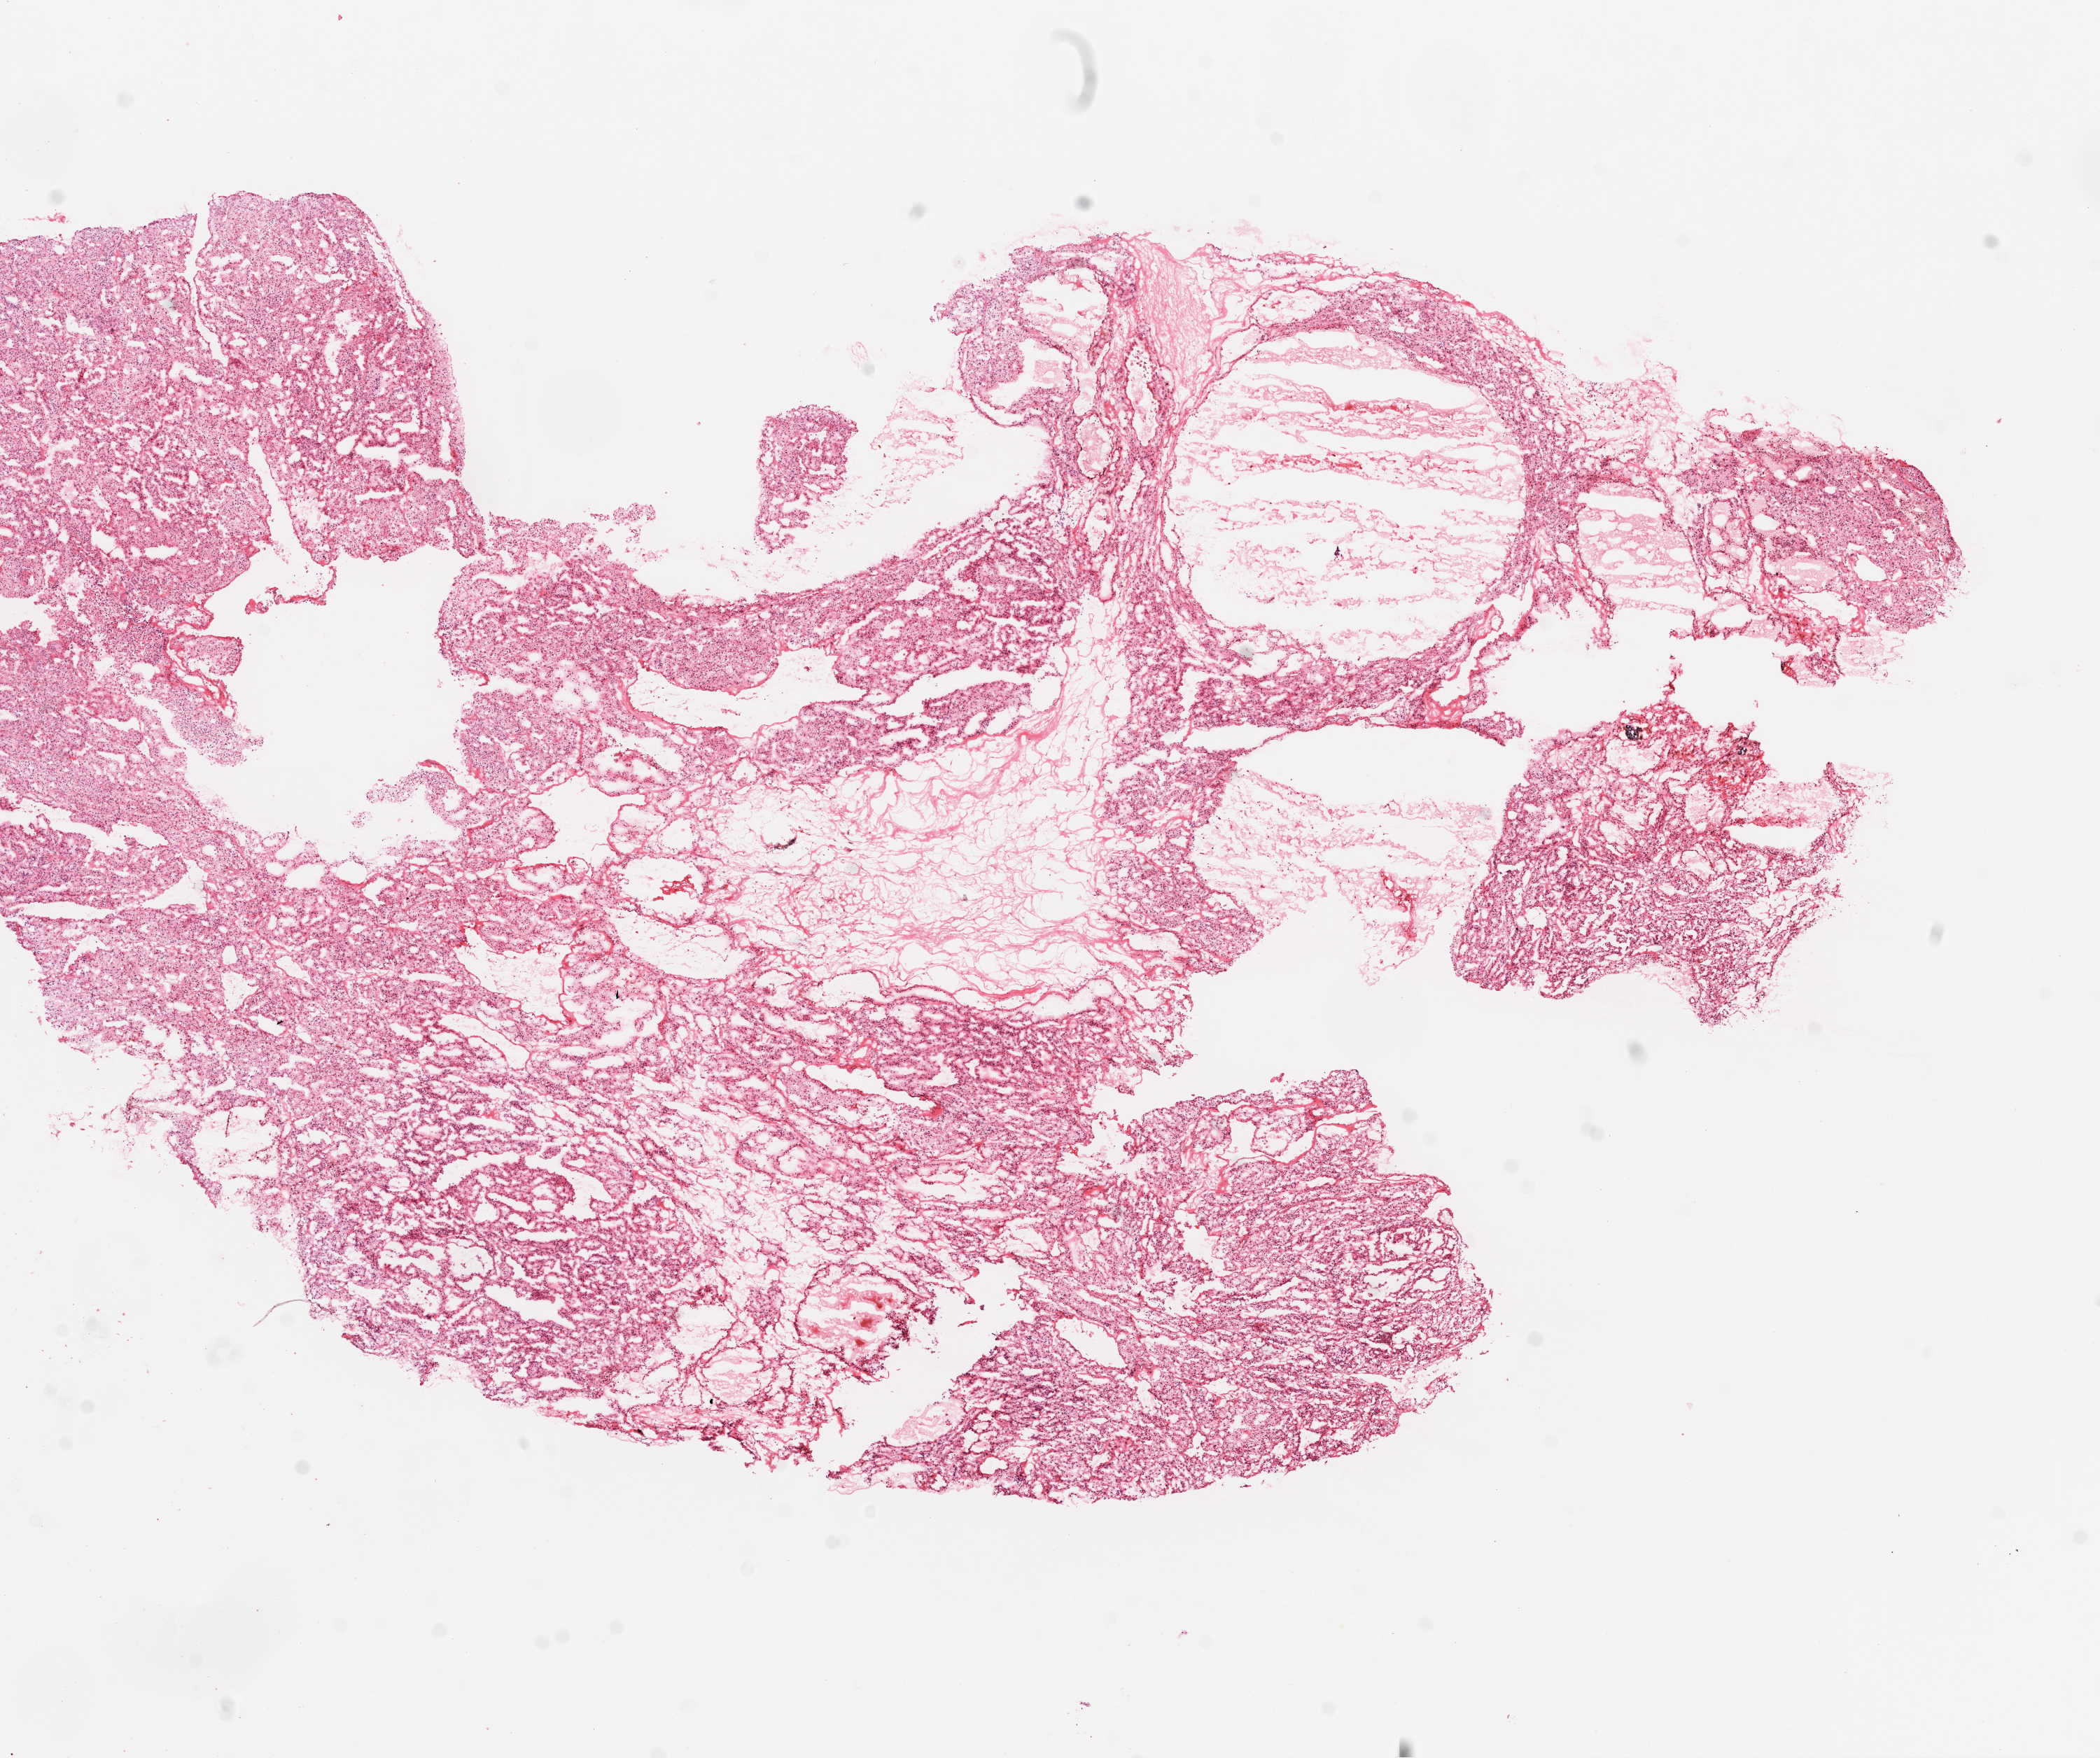
Whole-slide histology image, Hematoxylin and eosin (H&E) stained — low-resolution overview of the scanned area, about 12.0 x 10.1 mm (acquisition: 20x scan), frozen section from the top of the tissue portion, kidney, primary tumour sample. Patient: male, age at initial diagnosis 76 years. Histologic grade: G2 (moderately differentiated). Slide review estimates, as recorded: tumour cells 85%, tumour nuclei 85%, normal cells 0%, stromal cells 15%, necrosis 0%.
* AJCC pathologic stage: II
* pathologic diagnosis: Clear cell adenocarcinoma, NOS
* TNM: T2 NX M0